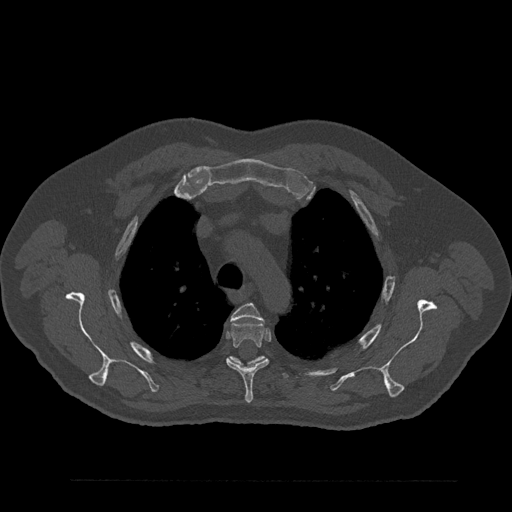
CT including the spine, one axial slice; slice 641 of 797 in the series (ordered by position); 120 kVp; bone window (W 1800 / L 400 HU); 0.5 mm slice thickness; 512 × 512 image matrix, field of view 430 × 430 mm. Patient: male, 61 years. From the clinical record (not read from this slice): primary cancer: prostate.
Structures marked on this image (semi-automatic segmentation, software-assisted and operator-edited):
- T3 vertebra: bounding box (x1, y1, x2, y2) in pixels: (231, 303, 263, 320)
- T4 vertebra: (226, 322, 269, 403)
- T5 vertebra: (229, 356, 289, 379)